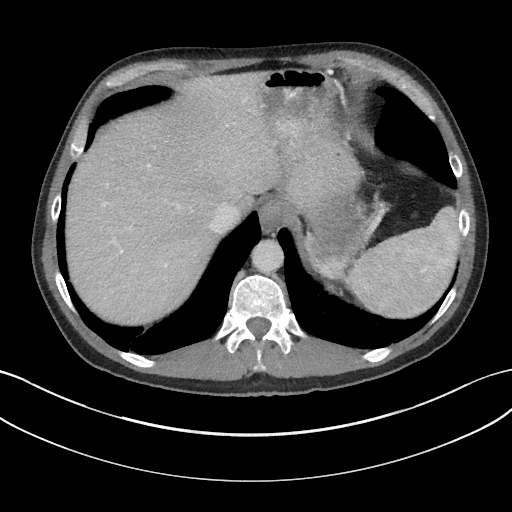
Contrast-enhanced abdominal CT, one axial slice. Slice 131 of 147 in the series (ordered by position). 100 kVp. Intravenous contrast given. Soft-tissue window (W 400 / L 40 HU). 3 mm slice thickness. 512 × 512 image matrix. Patient: male, 58 years. From the clinical record (not read from this slice): diagnosis: adrenocortical carcinoma; tumour side: left adrenal; tumour size at pathology: 22 cm; Ki-67 index: 26 %; stage (as recorded): 2.
Structures marked on this image (semi-automatically segmented with operator editing):
- mass: bounding box [x1, y1, x2, y2] px = [312, 197, 361, 253]